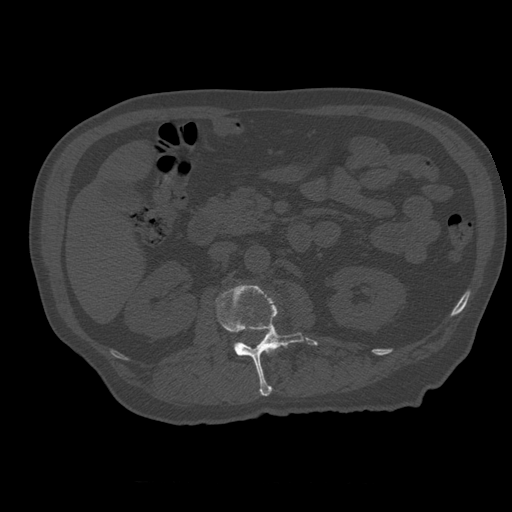
CT including the spine, one axial slice; position 213 of 399 along the scan axis; 120 kVp; bone window (W 1800 / L 400 HU); 1.25 mm slice thickness; 512 × 512 image matrix, field of view 407 × 407 mm. Patient age 73 years. From the clinical record (not read from this slice): primary cancer: prostate; vertebrae with lytic lesions (as recorded): L2.
Structures marked on this image (semi-automatically segmented with operator editing):
- L1 vertebra: bounding box (x1, y1, x2, y2) in pixels: (265, 348, 278, 354)
- L2 vertebra: (215, 285, 304, 396)